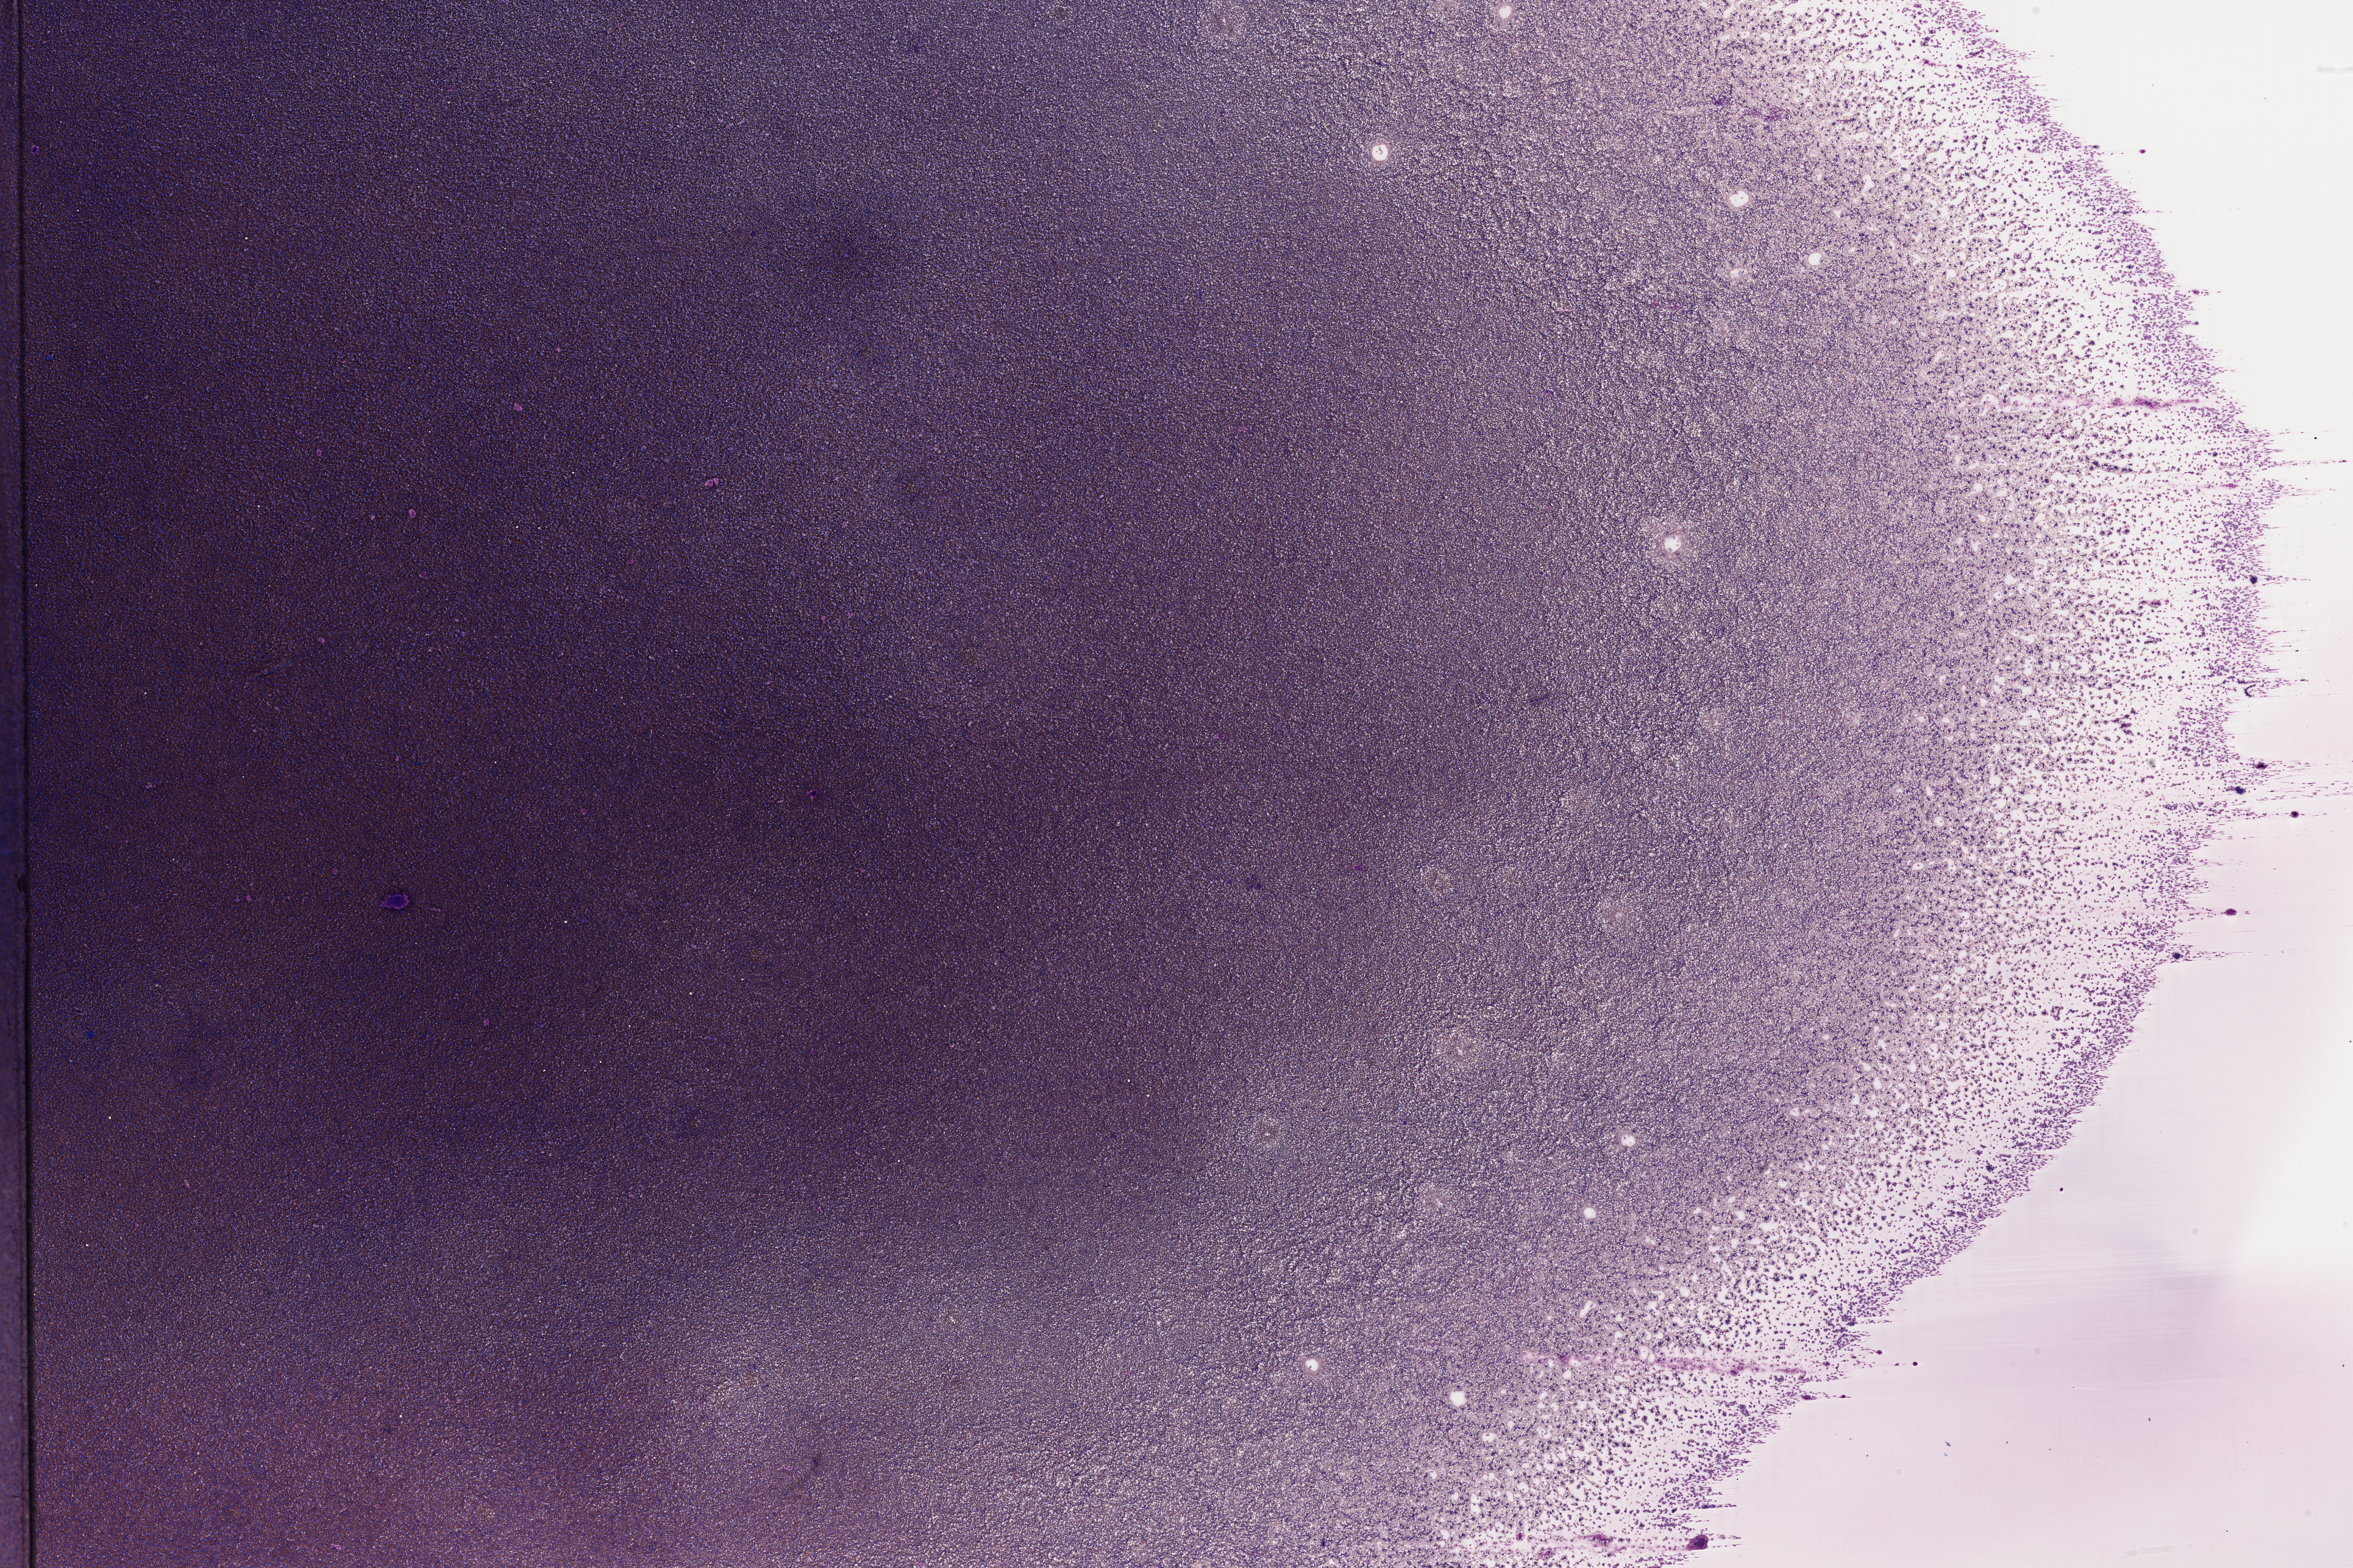
Whole-slide image, Wright-Giemsa stain — a low-resolution overview of the entire scanned area, about 30.7 x 20.5 mm; frozen section (tissue freezing medium); primary tumor; site: bone marrow. Patient: male, aged 11.
Histologic diagnosis: Burkitt lymphoma, NOS.